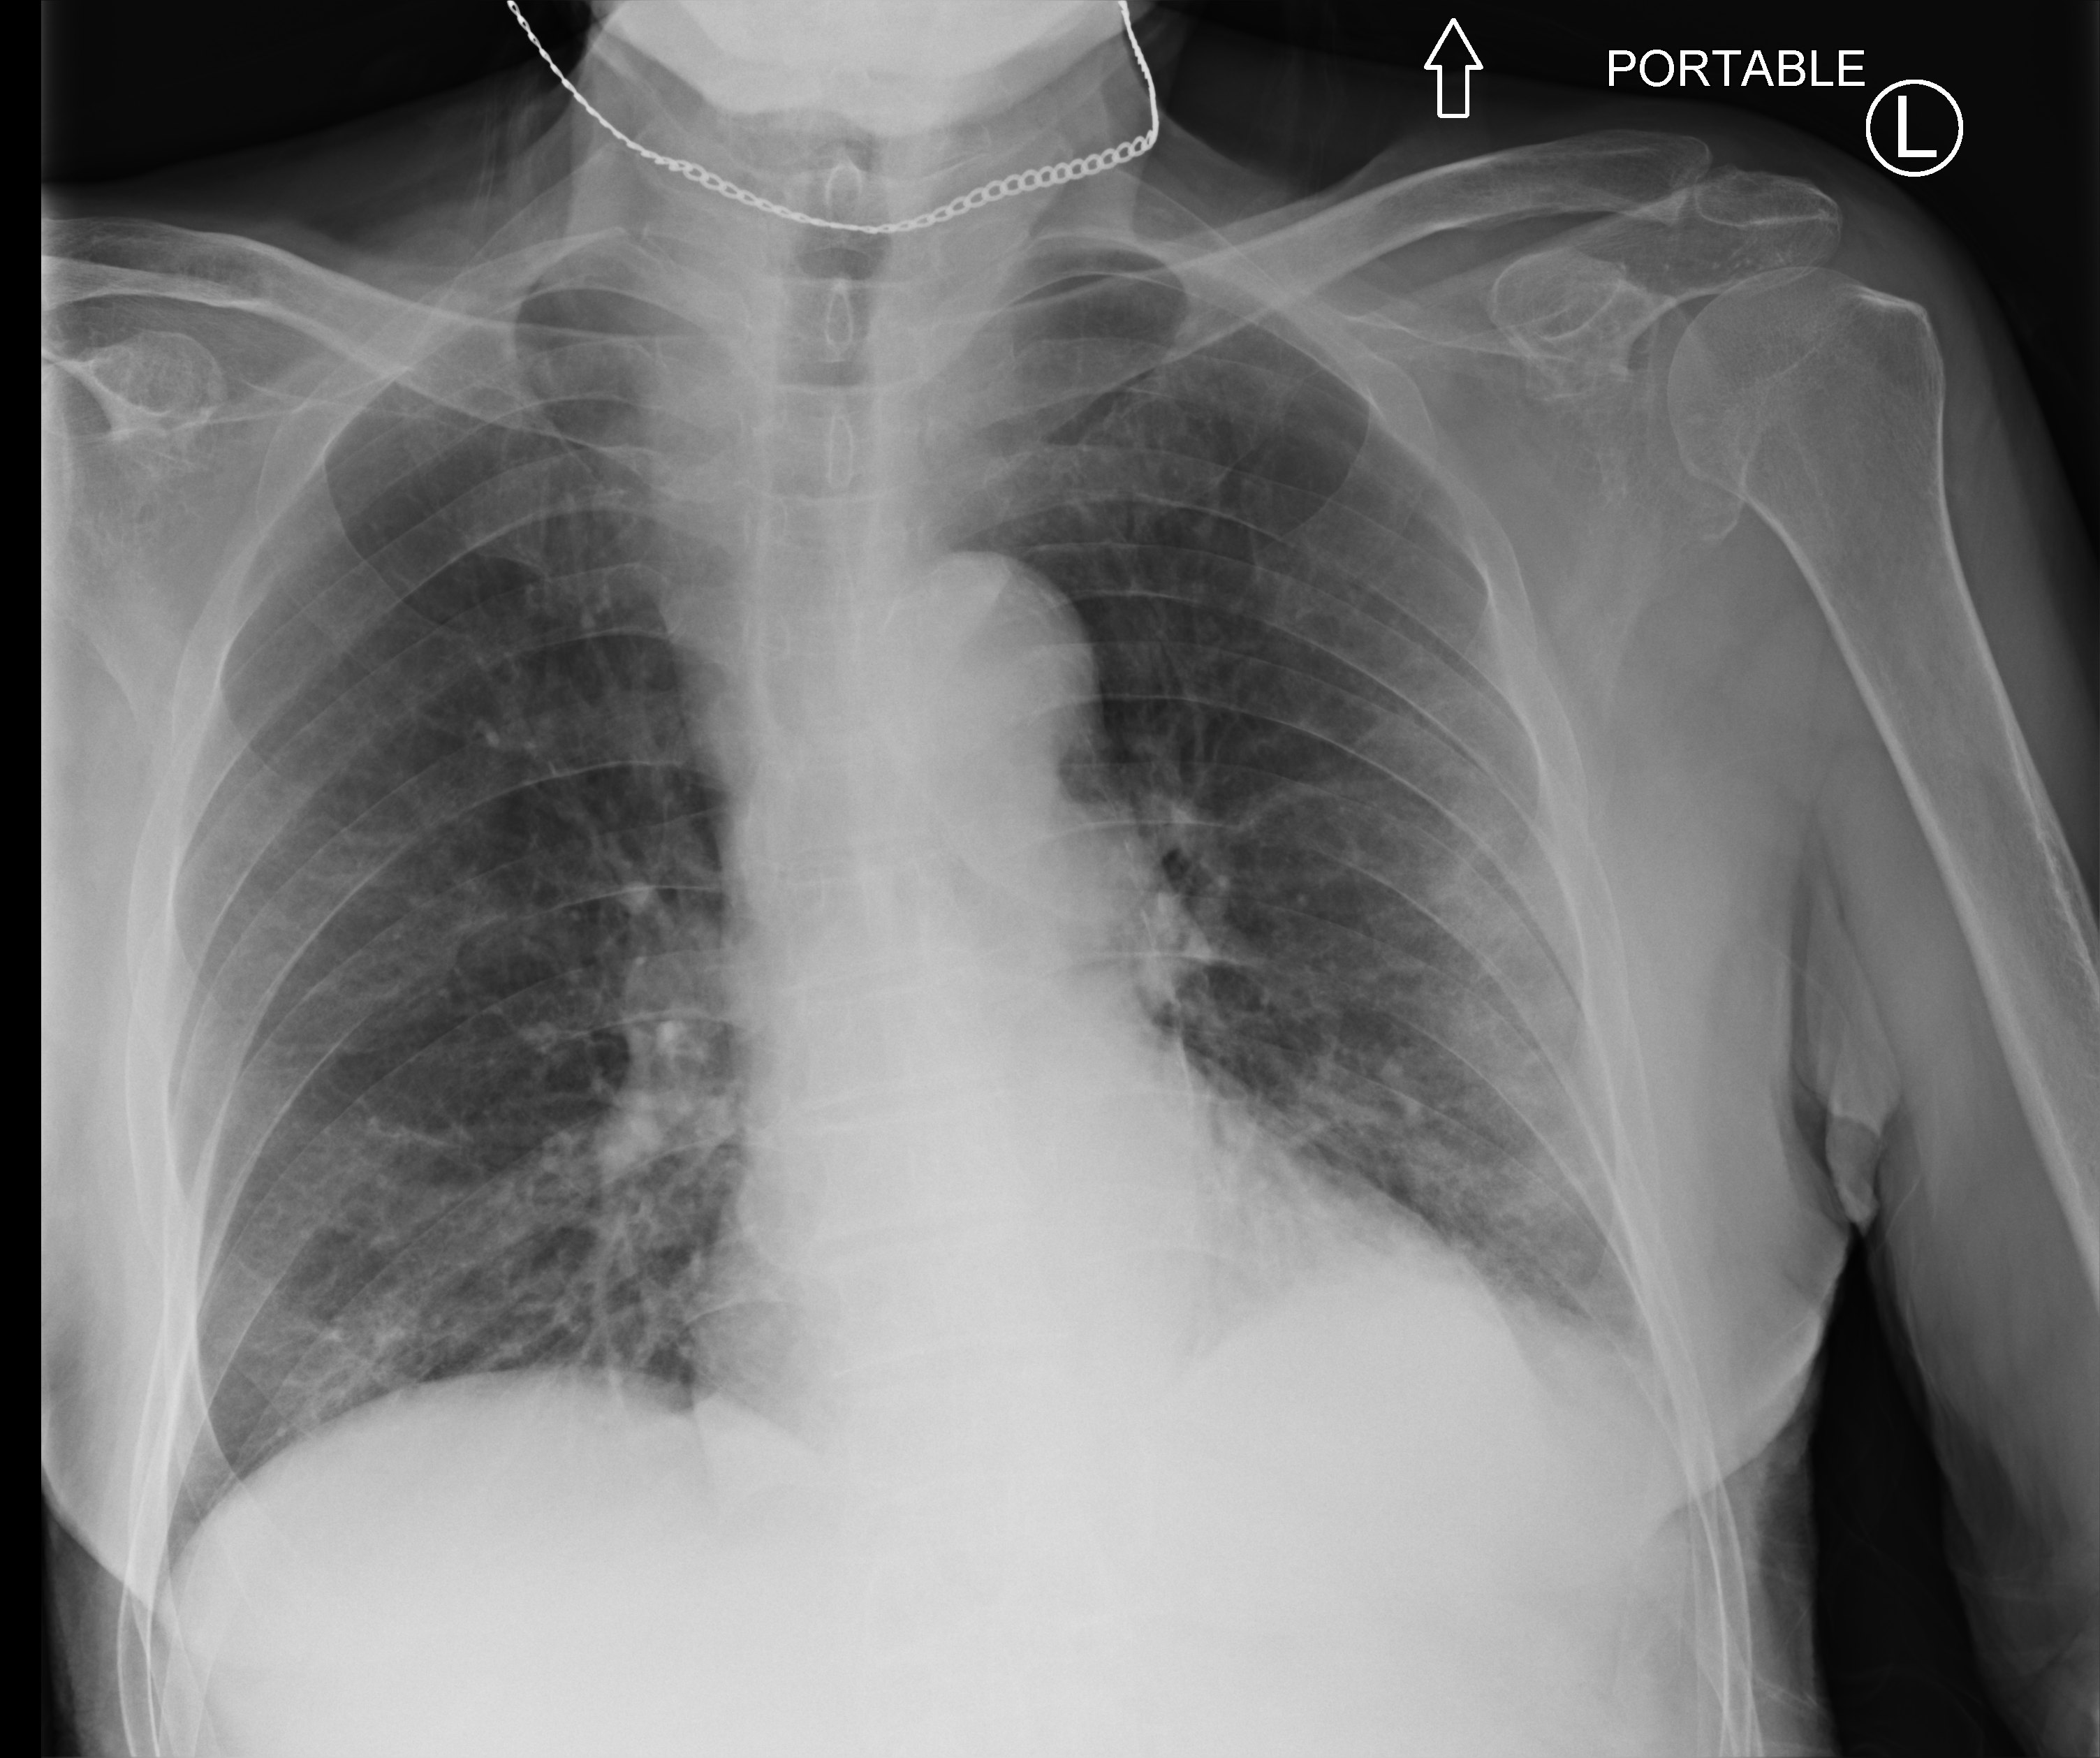
Portable chest radiograph; anteroposterior (AP) projection. Patient hospitalised with COVID-19; male, aged 75–90 years.
From the hospital-stay record, not from the radiograph (when in the stay this image was taken is not recorded):
- mechanically ventilated during this hospital stay: no